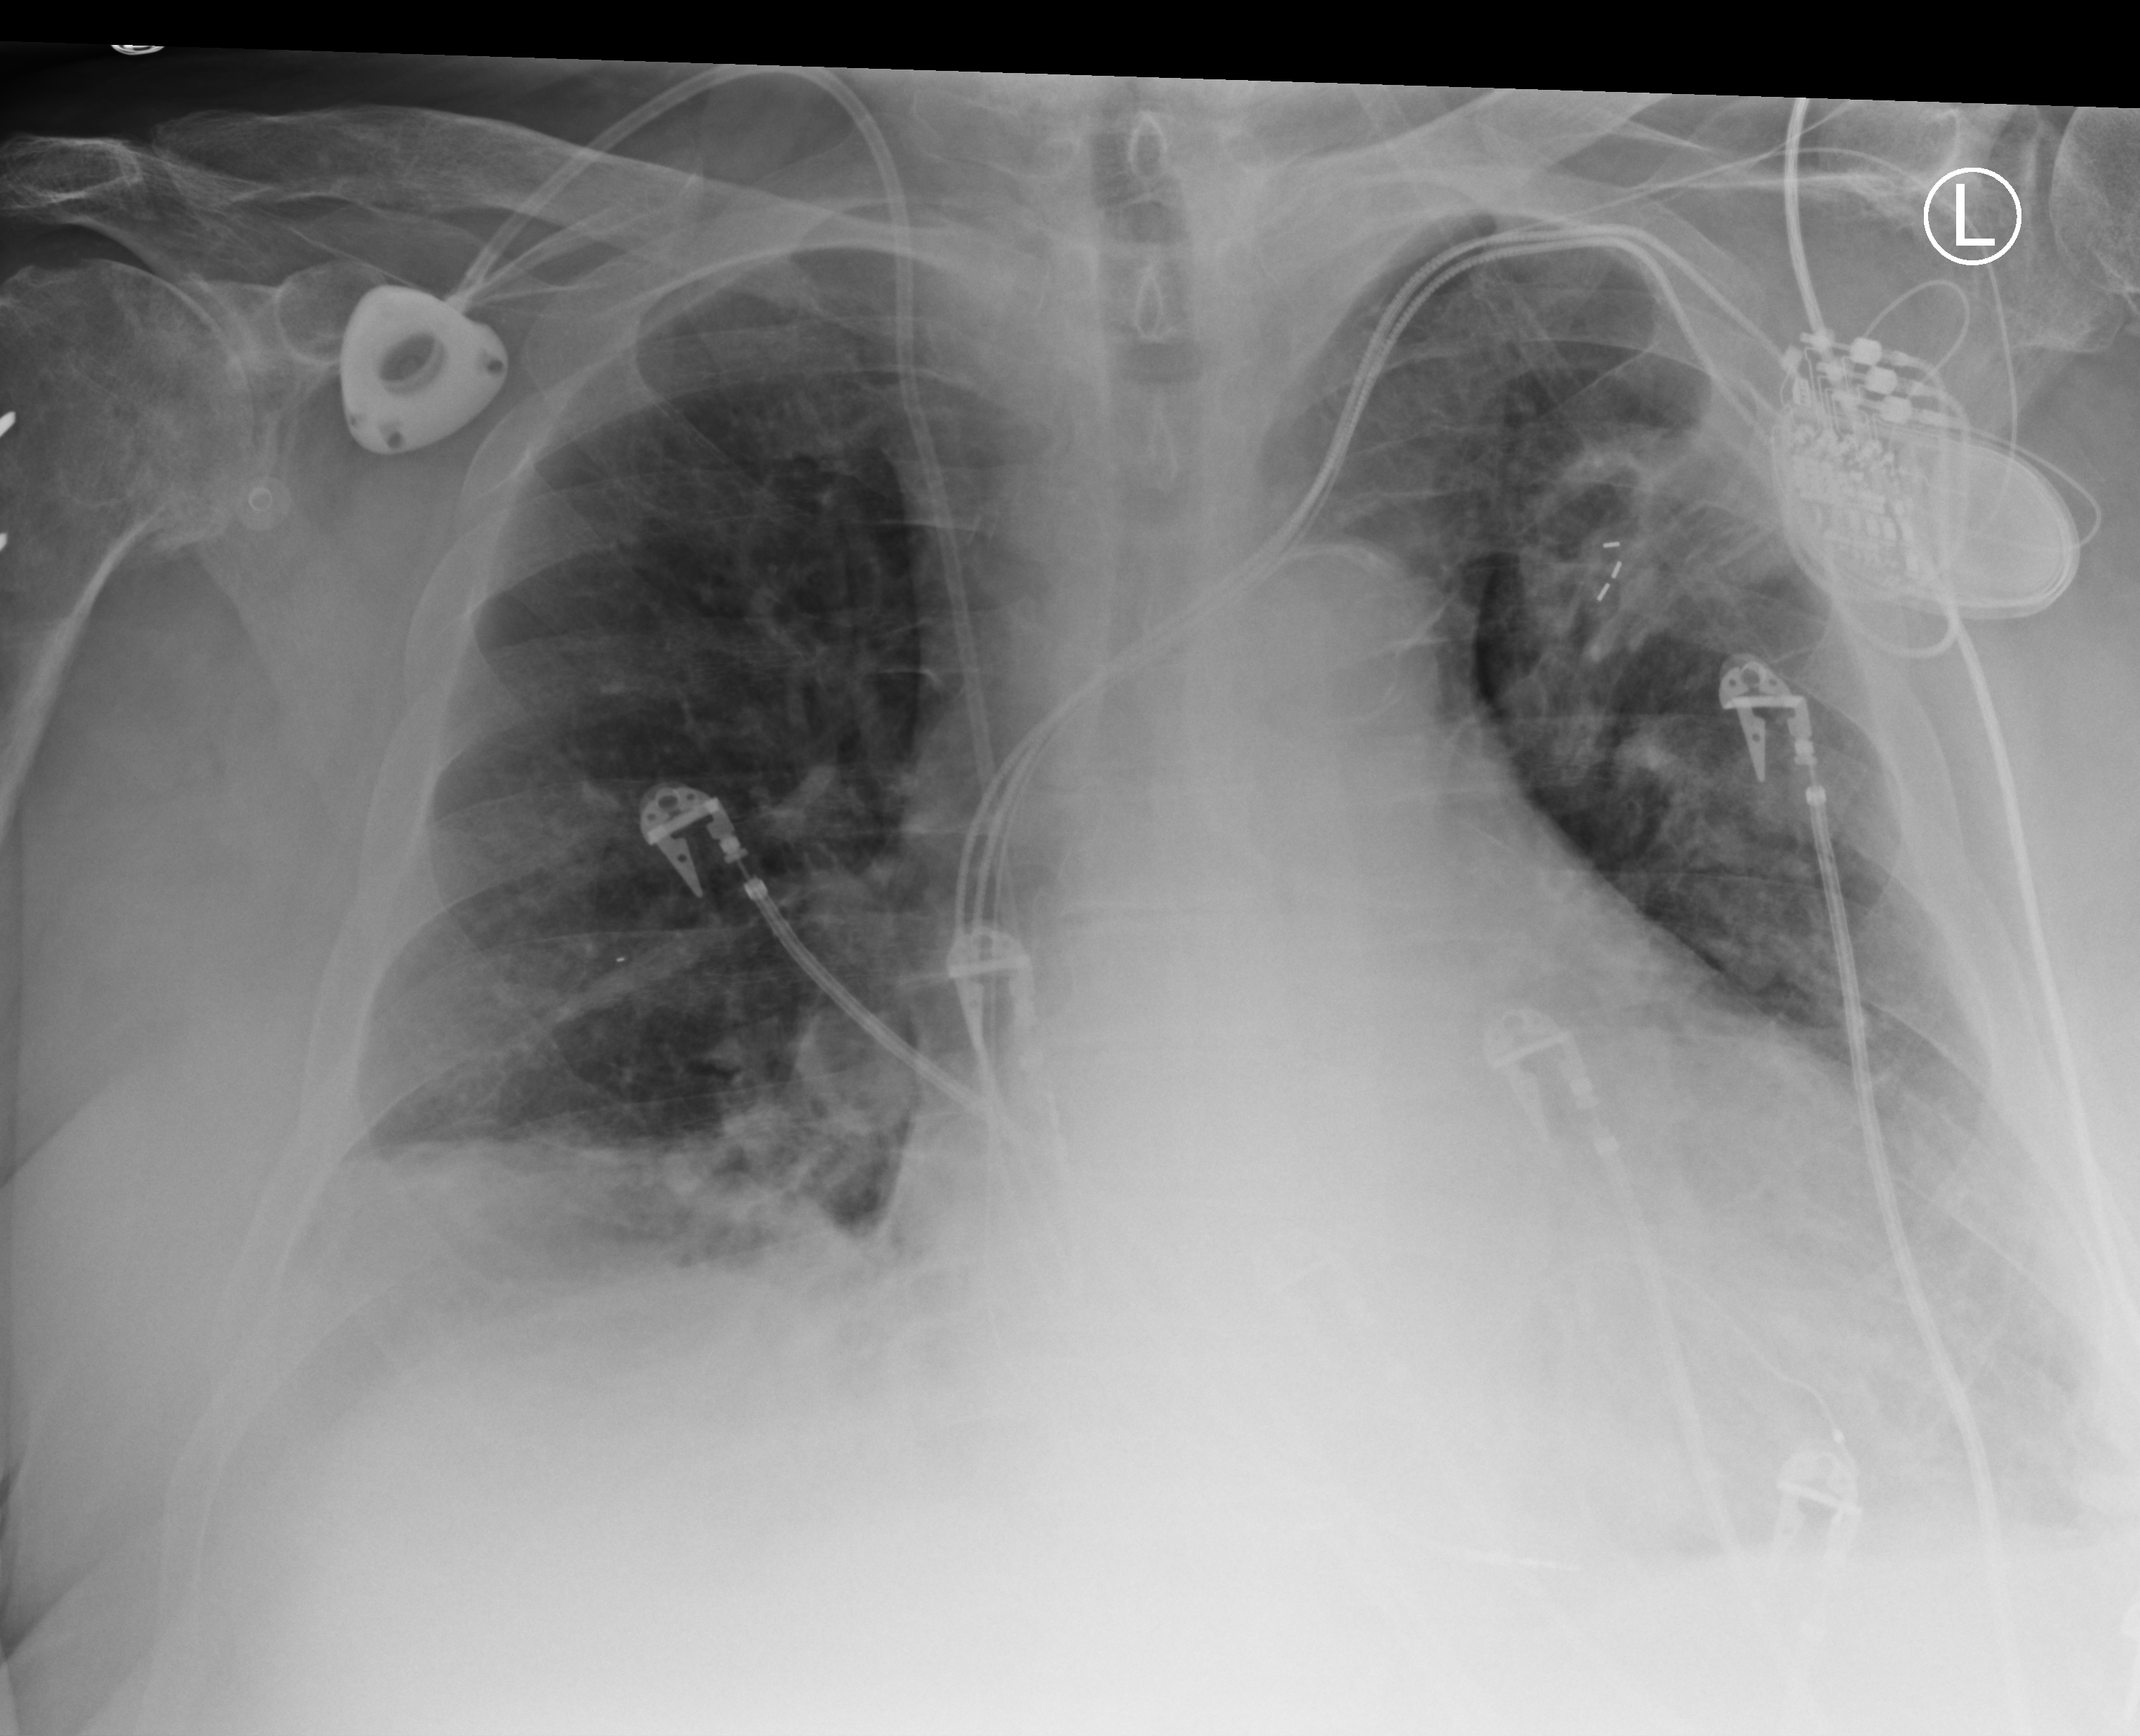
Chest X-ray (portable). Patient hospitalised with COVID-19; male, aged 60–74 years.
From the hospital-stay record, not from the radiograph (when in the stay this image was taken is not recorded): length of hospital stay: 20 days; admitted to intensive care during this hospital stay: yes; mechanically ventilated during this hospital stay: no.